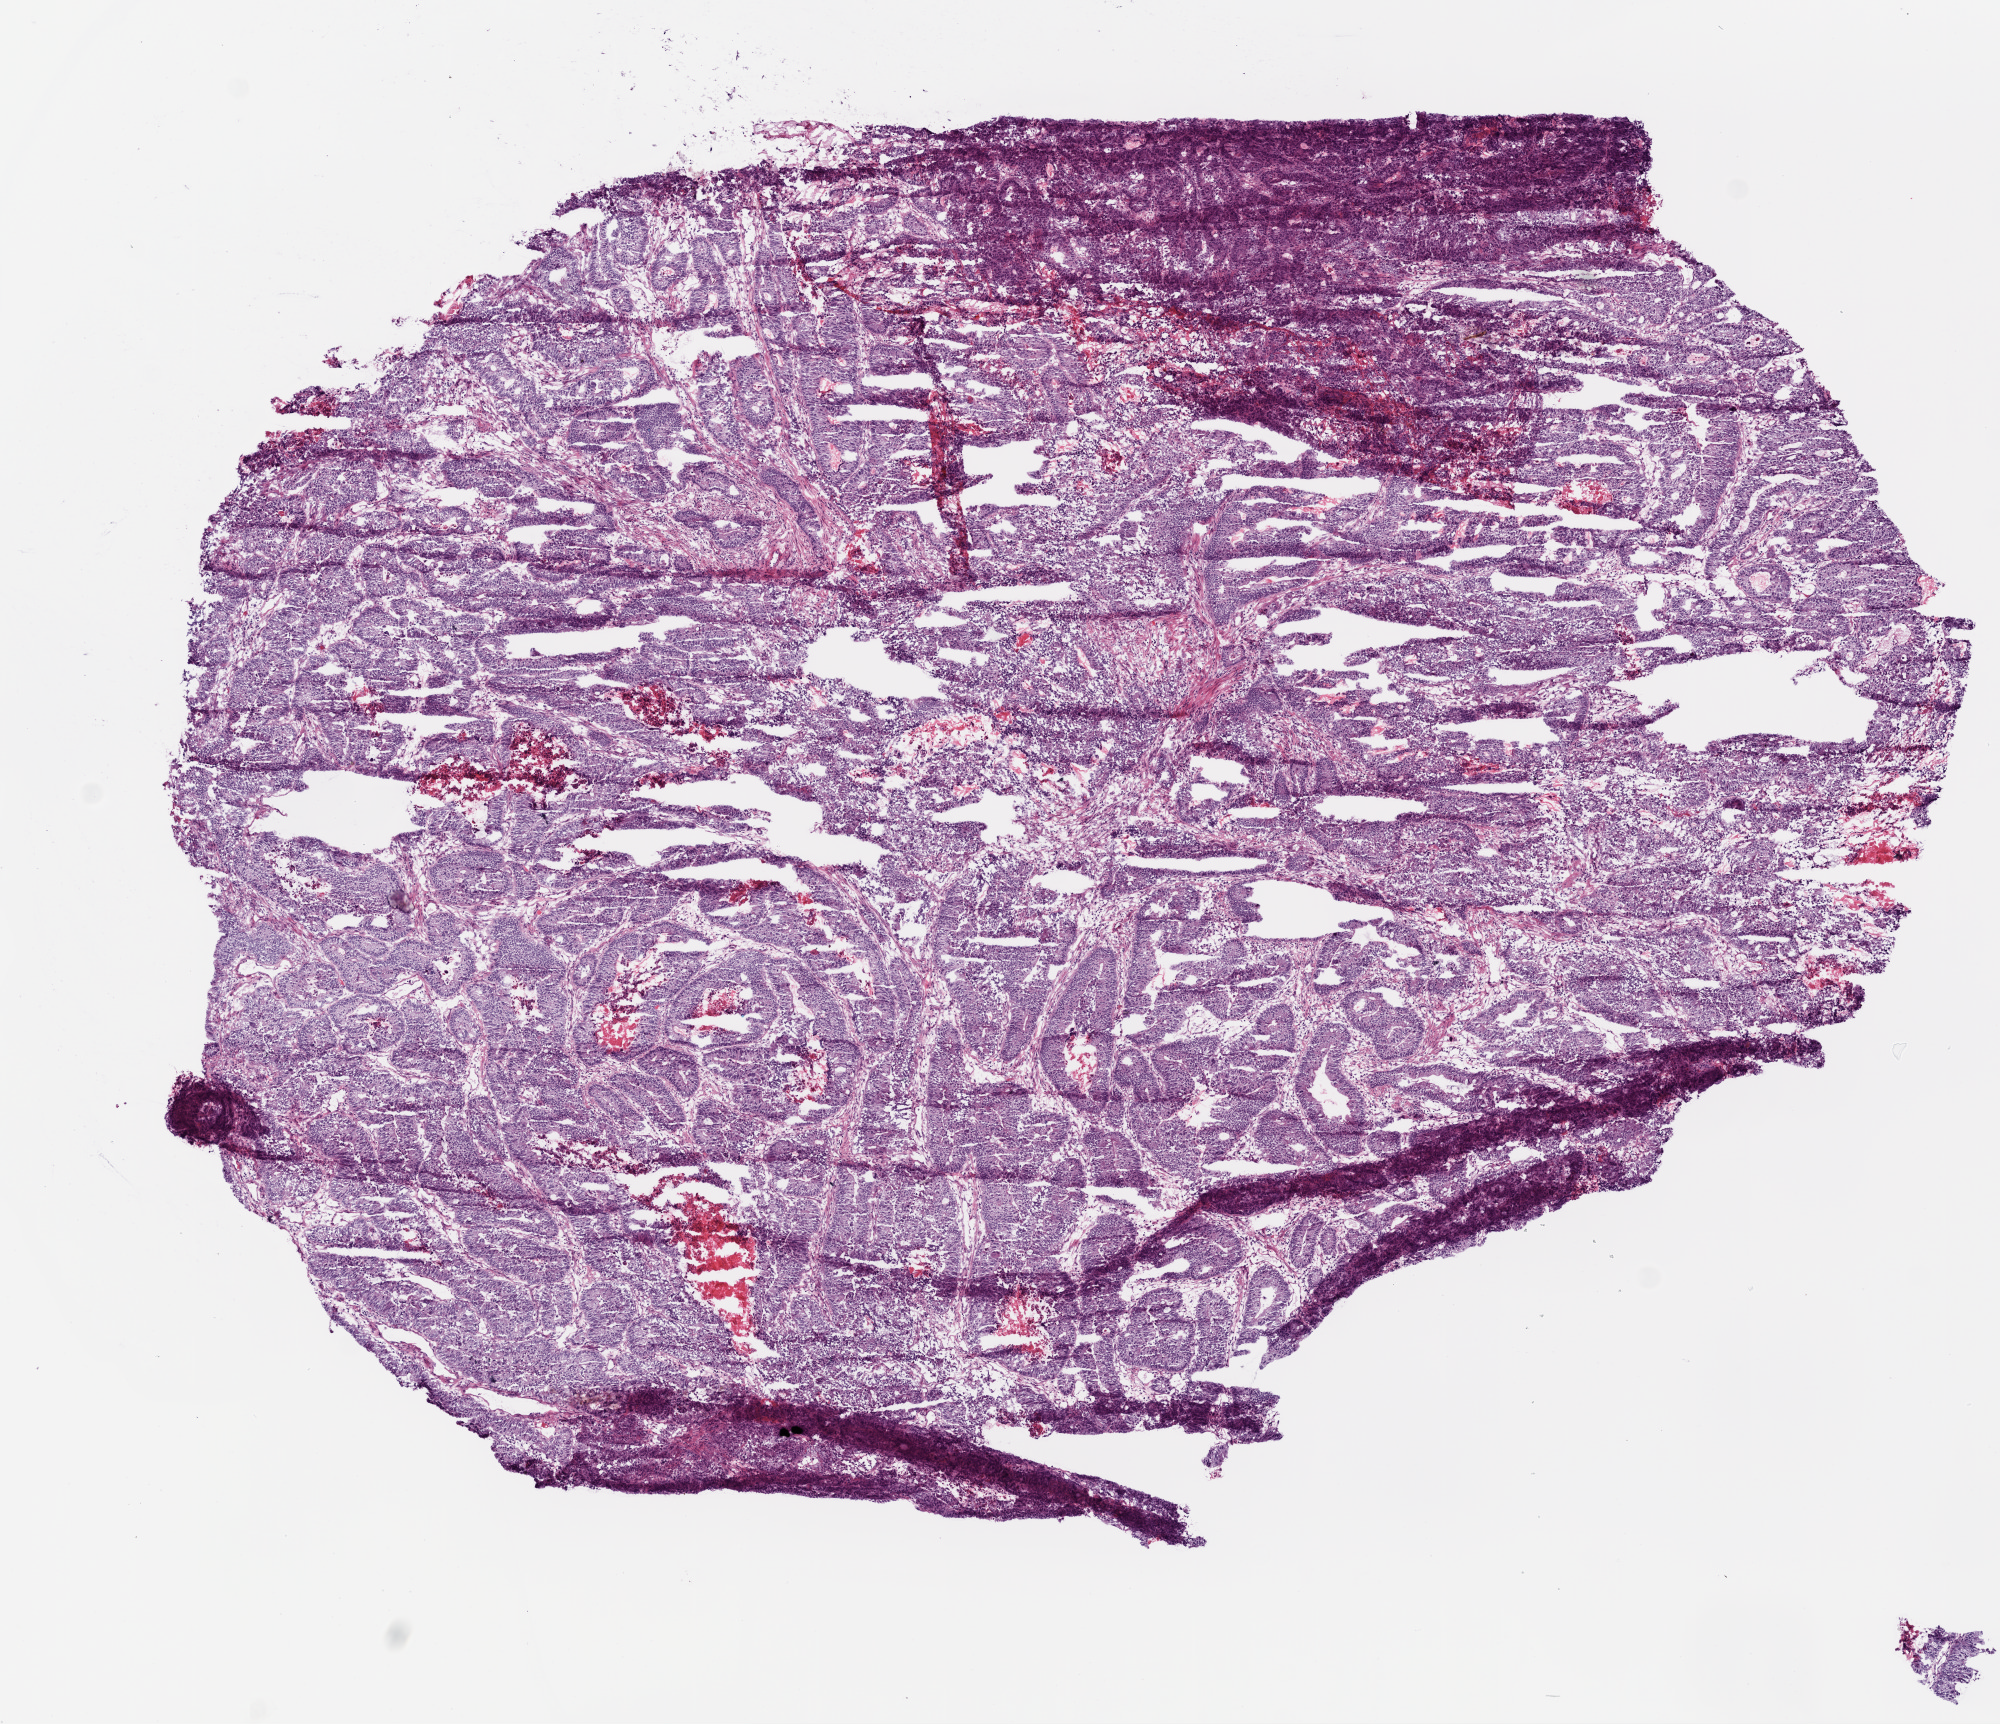
H&E-stained whole-slide image — whole scanned area (about 8.0 x 6.9 mm, from a 20x scan) shown as a low-resolution overview. Frozen section from the top of the tissue portion. Sample: primary tumour, colon. Male, age 72 years at initial diagnosis. Pathologist review of this section (percent, as recorded): tumour cells 80%, tumour nuclei 90%, normal cells 0%, stromal cells 20%, necrosis 0%.
• AJCC pathologic stage: IIA
• TNM: T3 N0 M0
• pathologic diagnosis: Adenocarcinoma, NOS